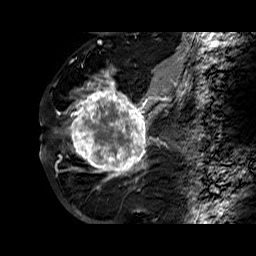
Breast MRI (dynamic contrast-enhanced), one sagittal slice. Slice 34 of 60 in the series (ordered by position). Dynamic contrast-enhanced series, time point 2 of 6 at this slice position (early post-contrast). 1.5 T. TE 6.3 ms, TR 32.4 ms. 256 × 256 image matrix. Female patient. Case-level facts recorded for this patient, not image findings: setting: breast cancer imaged before/during neoadjuvant chemotherapy; receptor status: HR-positive, HER2-negative.
Structures marked on this image (semi-automatic segmentation, software-assisted and operator-edited):
- analysis volume of interest (the breast-tissue region the enhancement analysis was run in; not a lesion): bounding box [x1, y1, x2, y2] px = [68, 72, 177, 183]
- tumour enhancement mask (voxels above the 100 % enhancement threshold inside the analysis volume of interest): [69, 72, 176, 181]